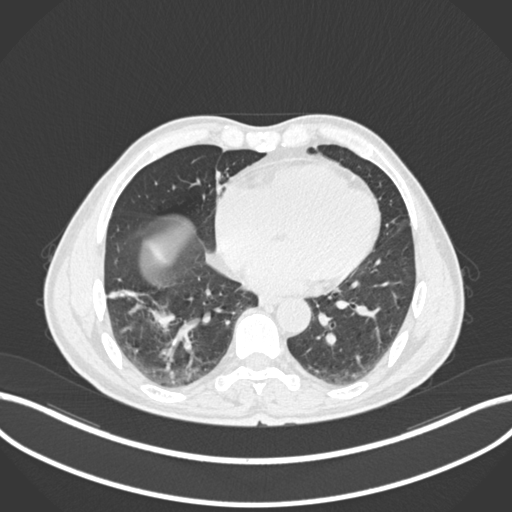
Chest CT, one axial slice; slice 57 of 208 in the series (ordered by position); lung window (W 1500 / L -600 HU); 1 mm slice thickness; 512 × 512 image matrix, field of view 400 × 400 mm. Patient: male, 58 years. Case-level facts recorded for this patient, not image findings: clinical TNM (as recorded): T3 N0 M0; histopathological grade: G2.
Structures marked on this image (bounding box drawn by a radiologist):
- lung tumour (recorded histology: squamous cell carcinoma): bounding box (x1, y1, x2, y2) in pixels: (101, 278, 176, 333)